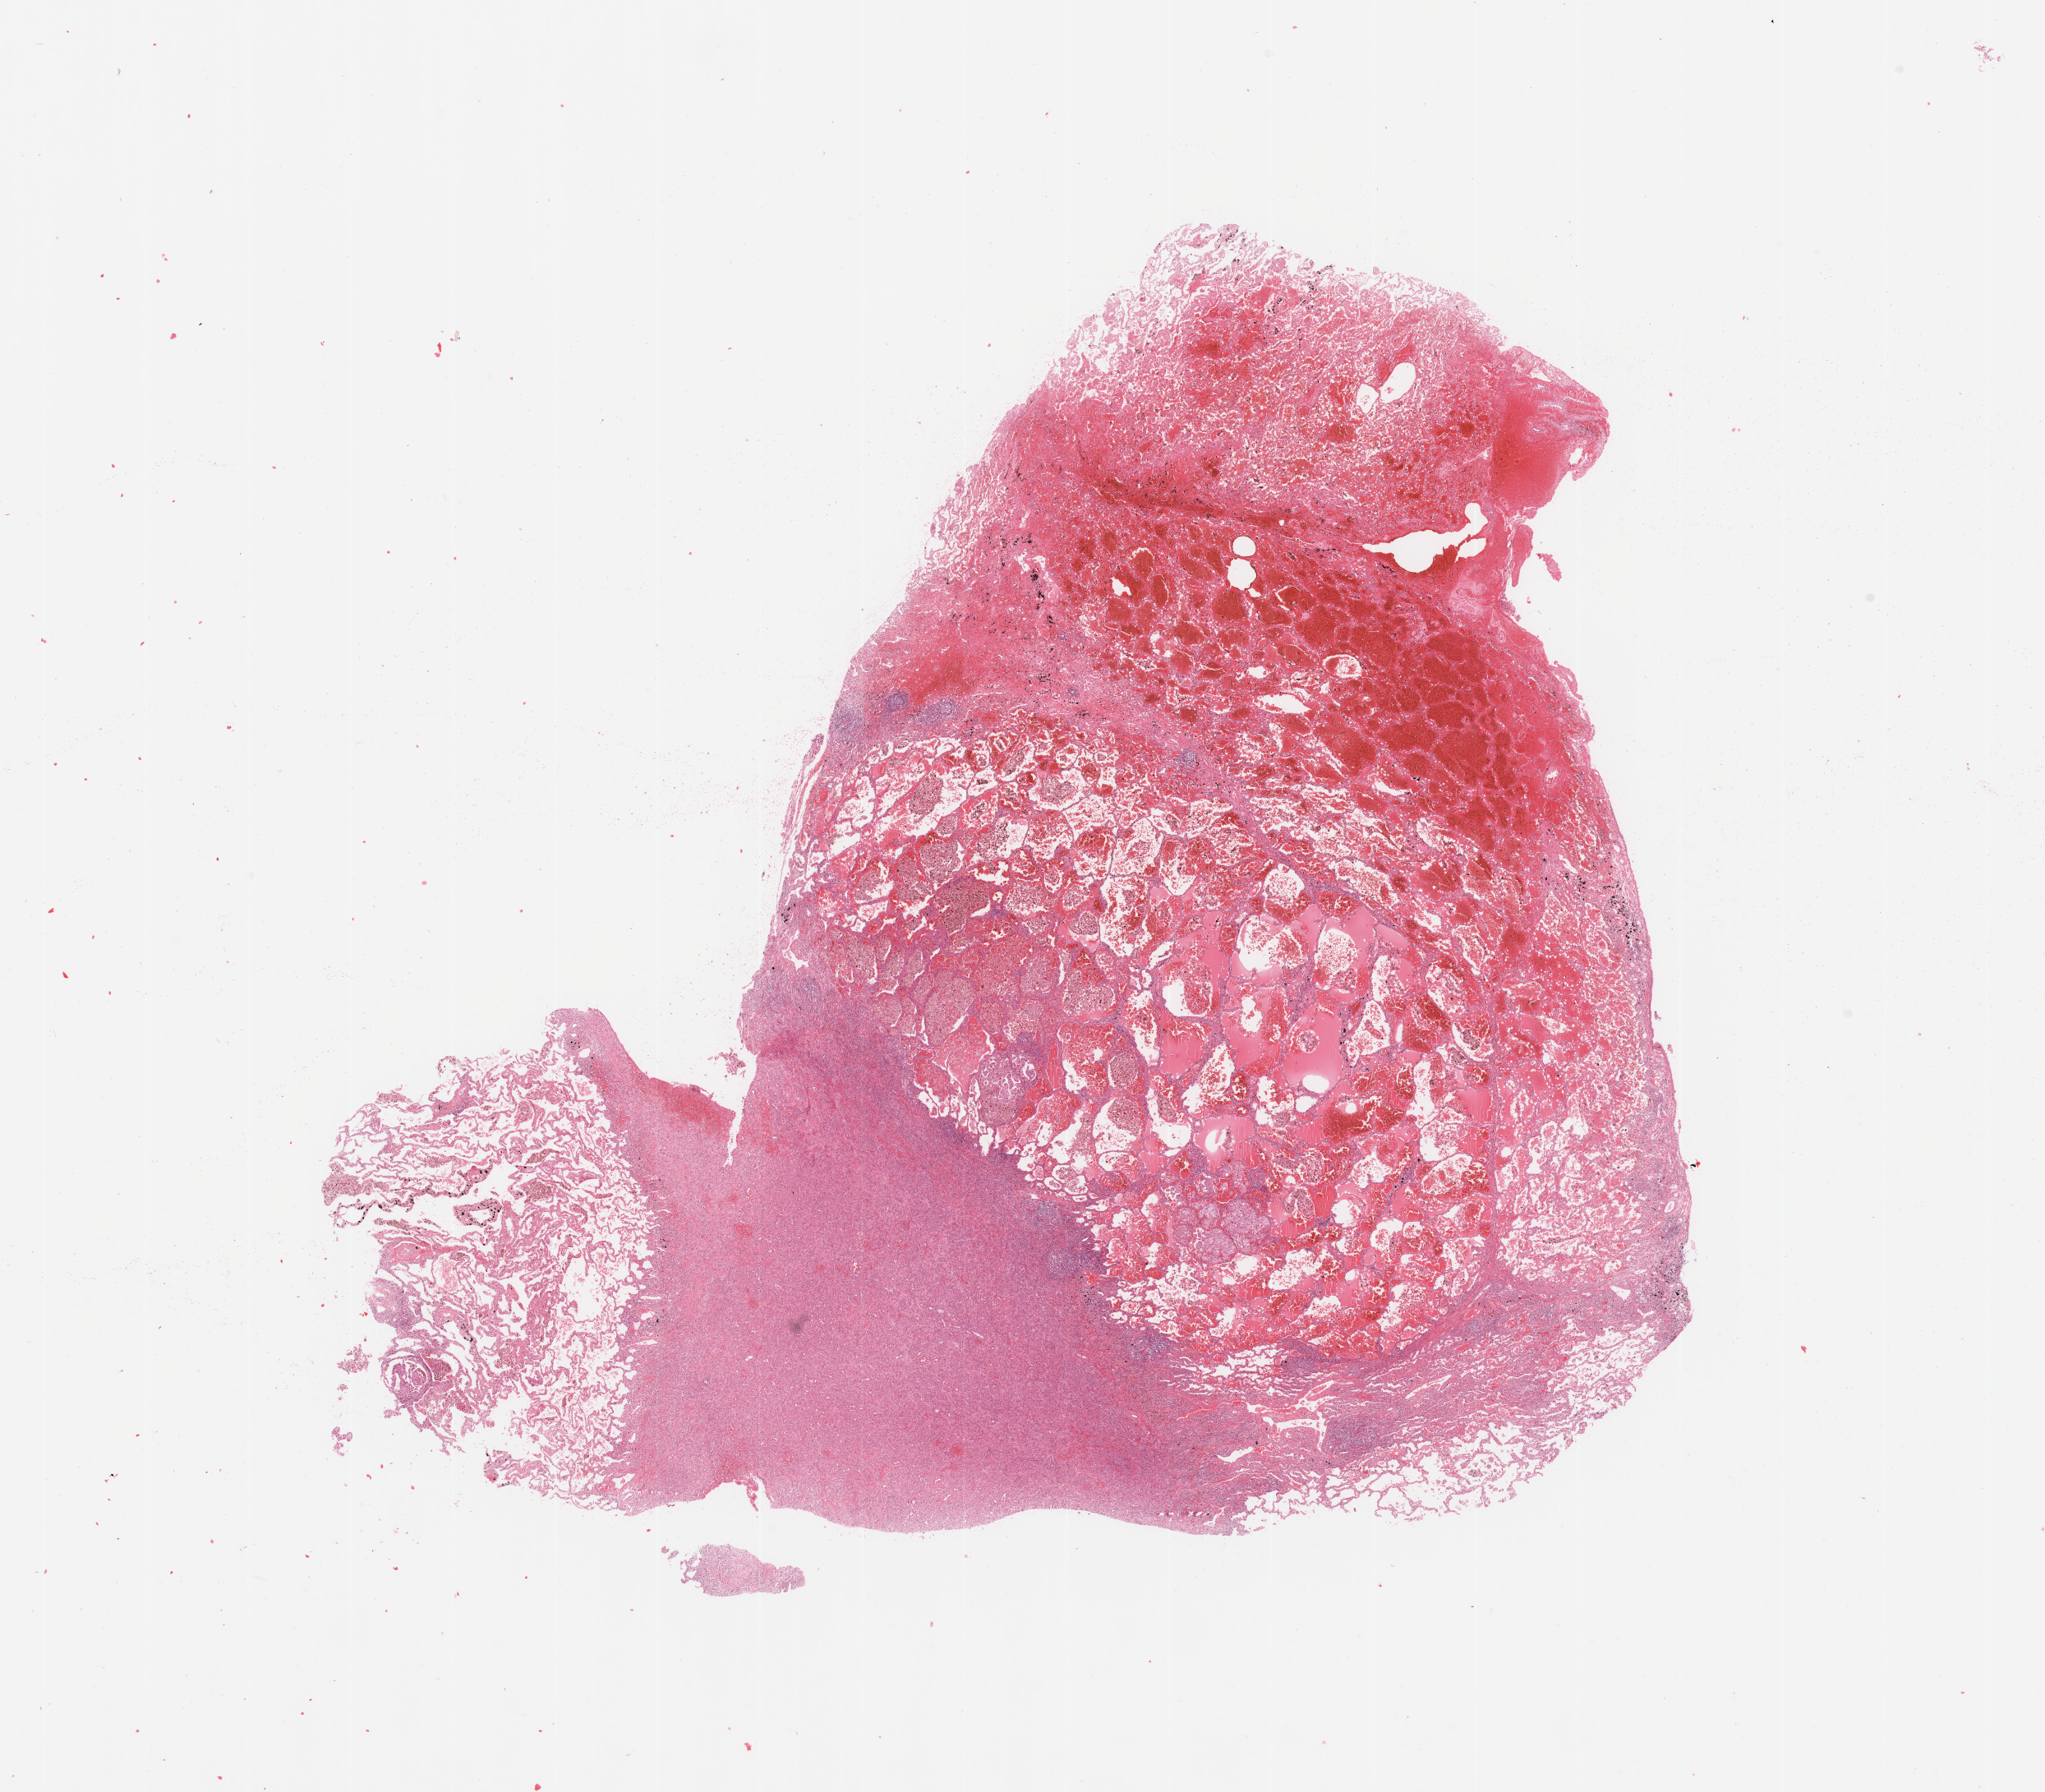
Digitized H&E tissue section (whole slide) — low-resolution overview of the scanned area, about 19.7 x 17.3 mm (from a 20x scan), lung, tumour tissue. Male, 48 y/o. Histologic grade: G2 (moderately differentiated).
Diagnosis: Adenocarcinoma, NOS. AJCC pathologic stage: IB. Primary tumour site (as recorded): right lower lobe.